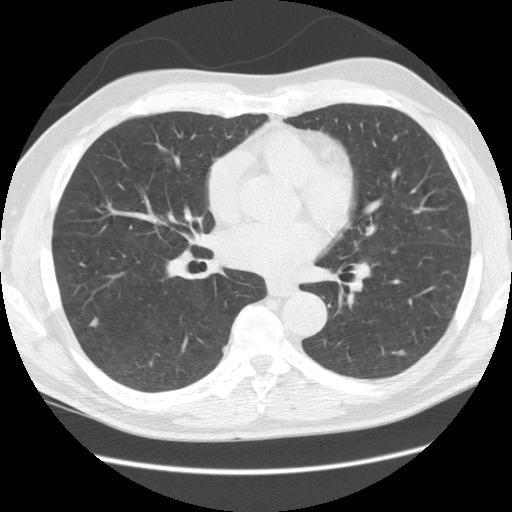
Low-dose screening chest CT, one axial slice. Slice 49 of 111 in the series (ordered by position). Reconstruction kernel STANDARD. 120 kVp. Lung window (W 1500 / L -600 HU). 2.5 mm slice thickness. 512 × 512 image matrix, field of view 370 × 370 mm.
Structures marked on this image (outlined manually by an expert reader):
- lesion 3 (nodule, lower lobe of right lung): bounding box <89,318,99,327> (left, top, right, bottom; pixels)